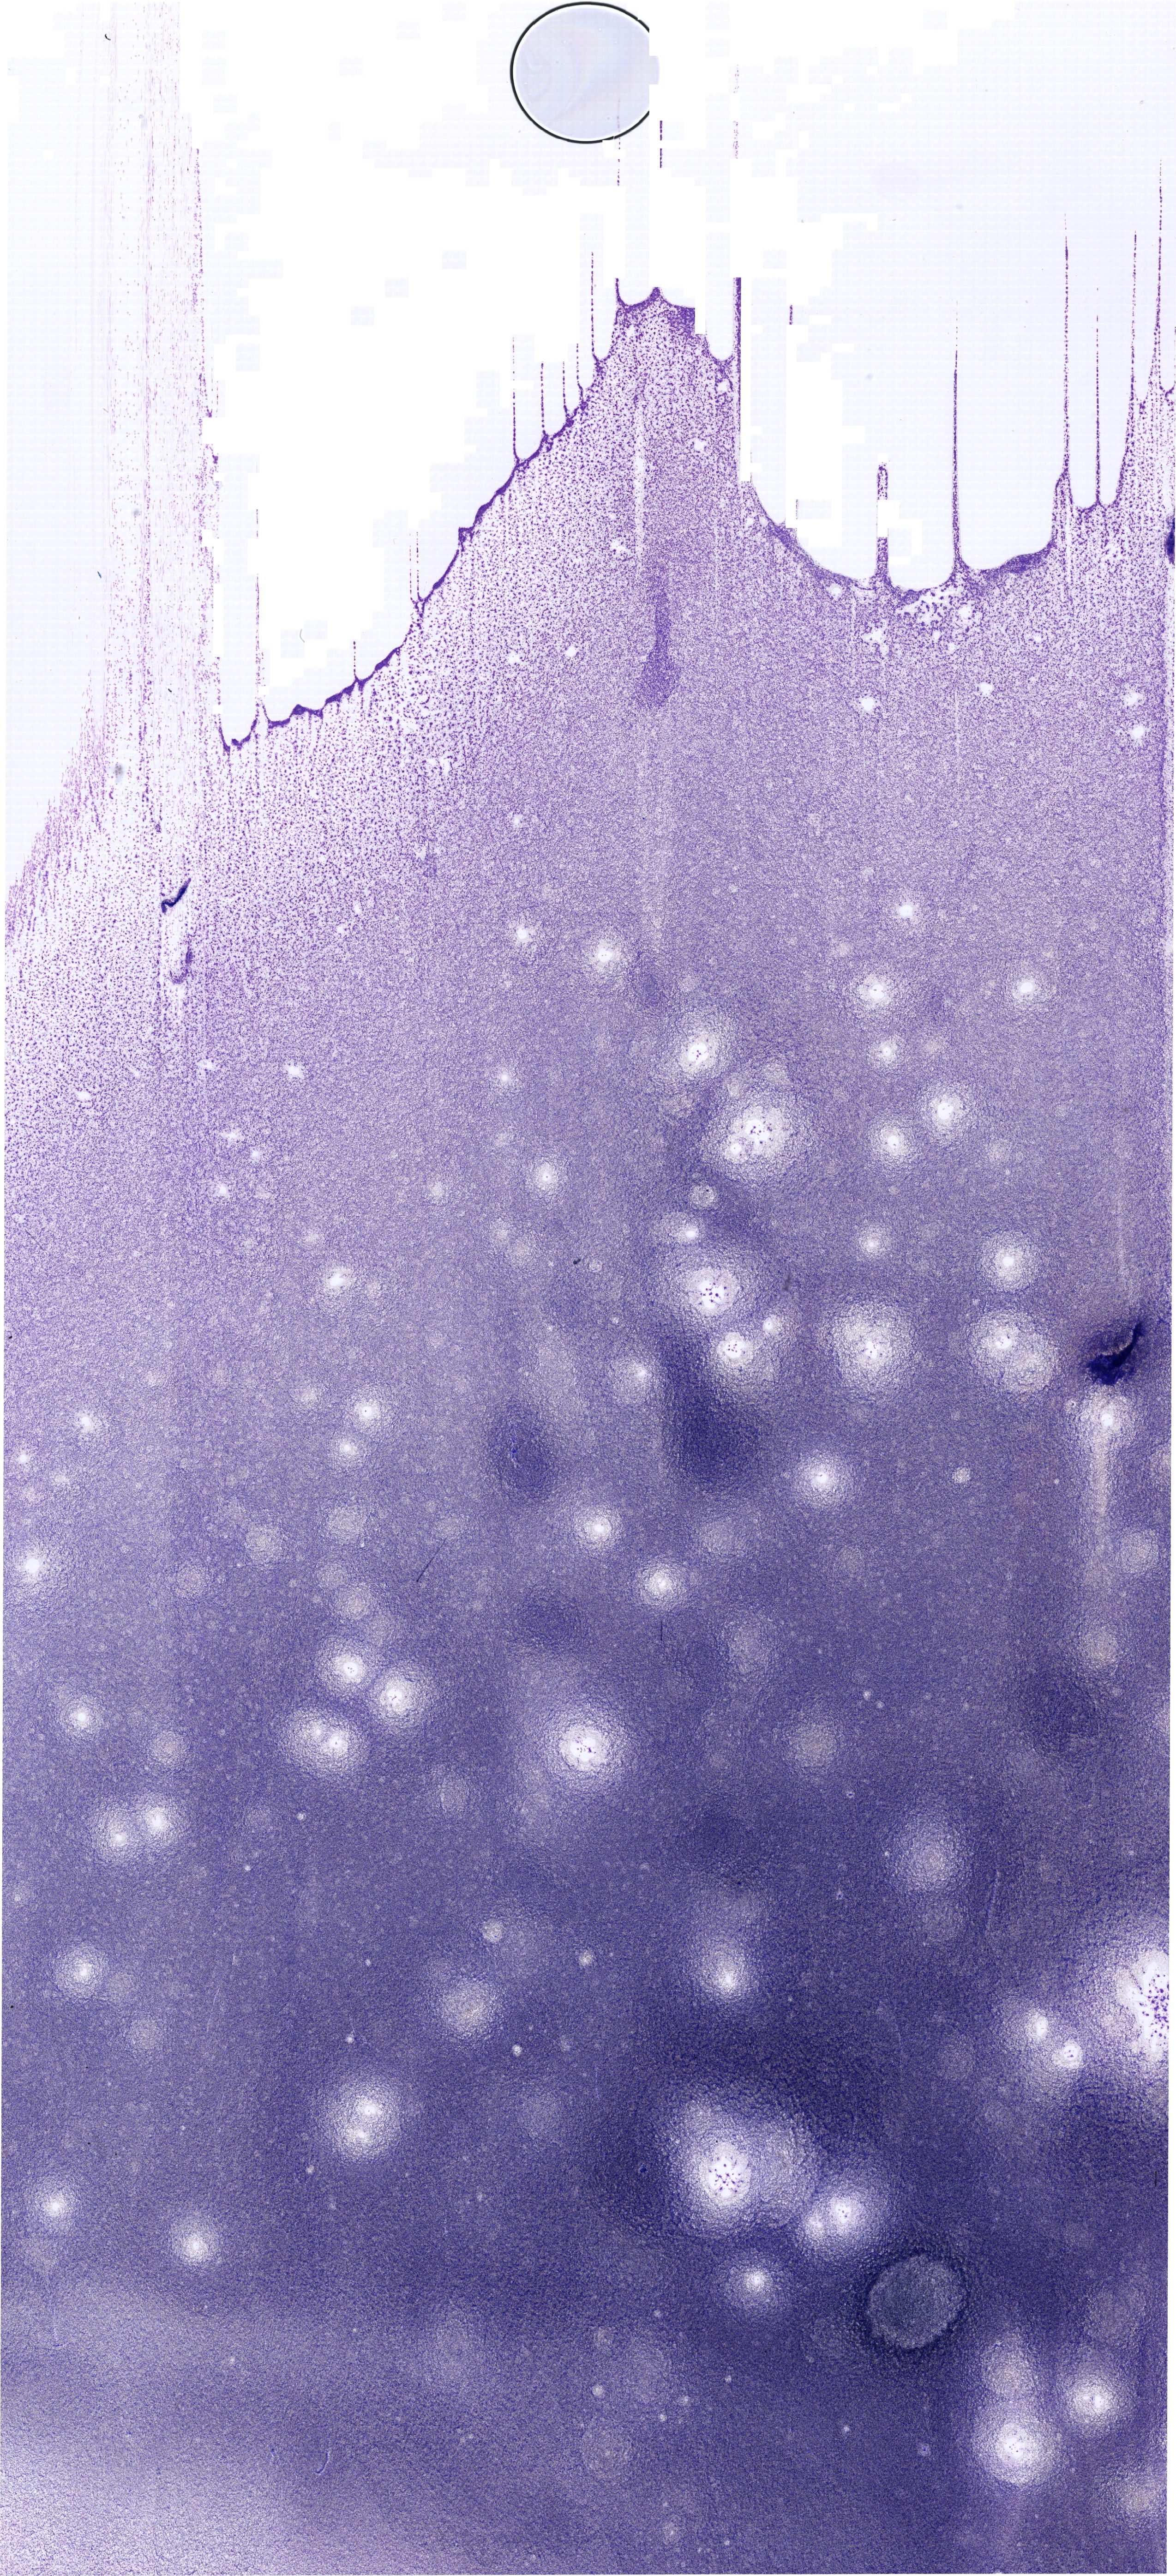
Whole-slide image of a May-Grünwald–Giemsa-stained bone marrow aspirate smear, shown as a low-resolution overview of the whole scanned area (about 19.9 x 43.6 mm). Female patient.
• diagnosis: Mixed Phenotype Acute Leukemia, B/Myeloid